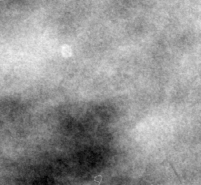
Region of interest cut from a scanned film mammogram (one marked finding), right breast, MLO view.
Finding: calcifications, morphology lucent center; BI-RADS assessment category 2; benign; no additional work-up was recommended (benign without callback).